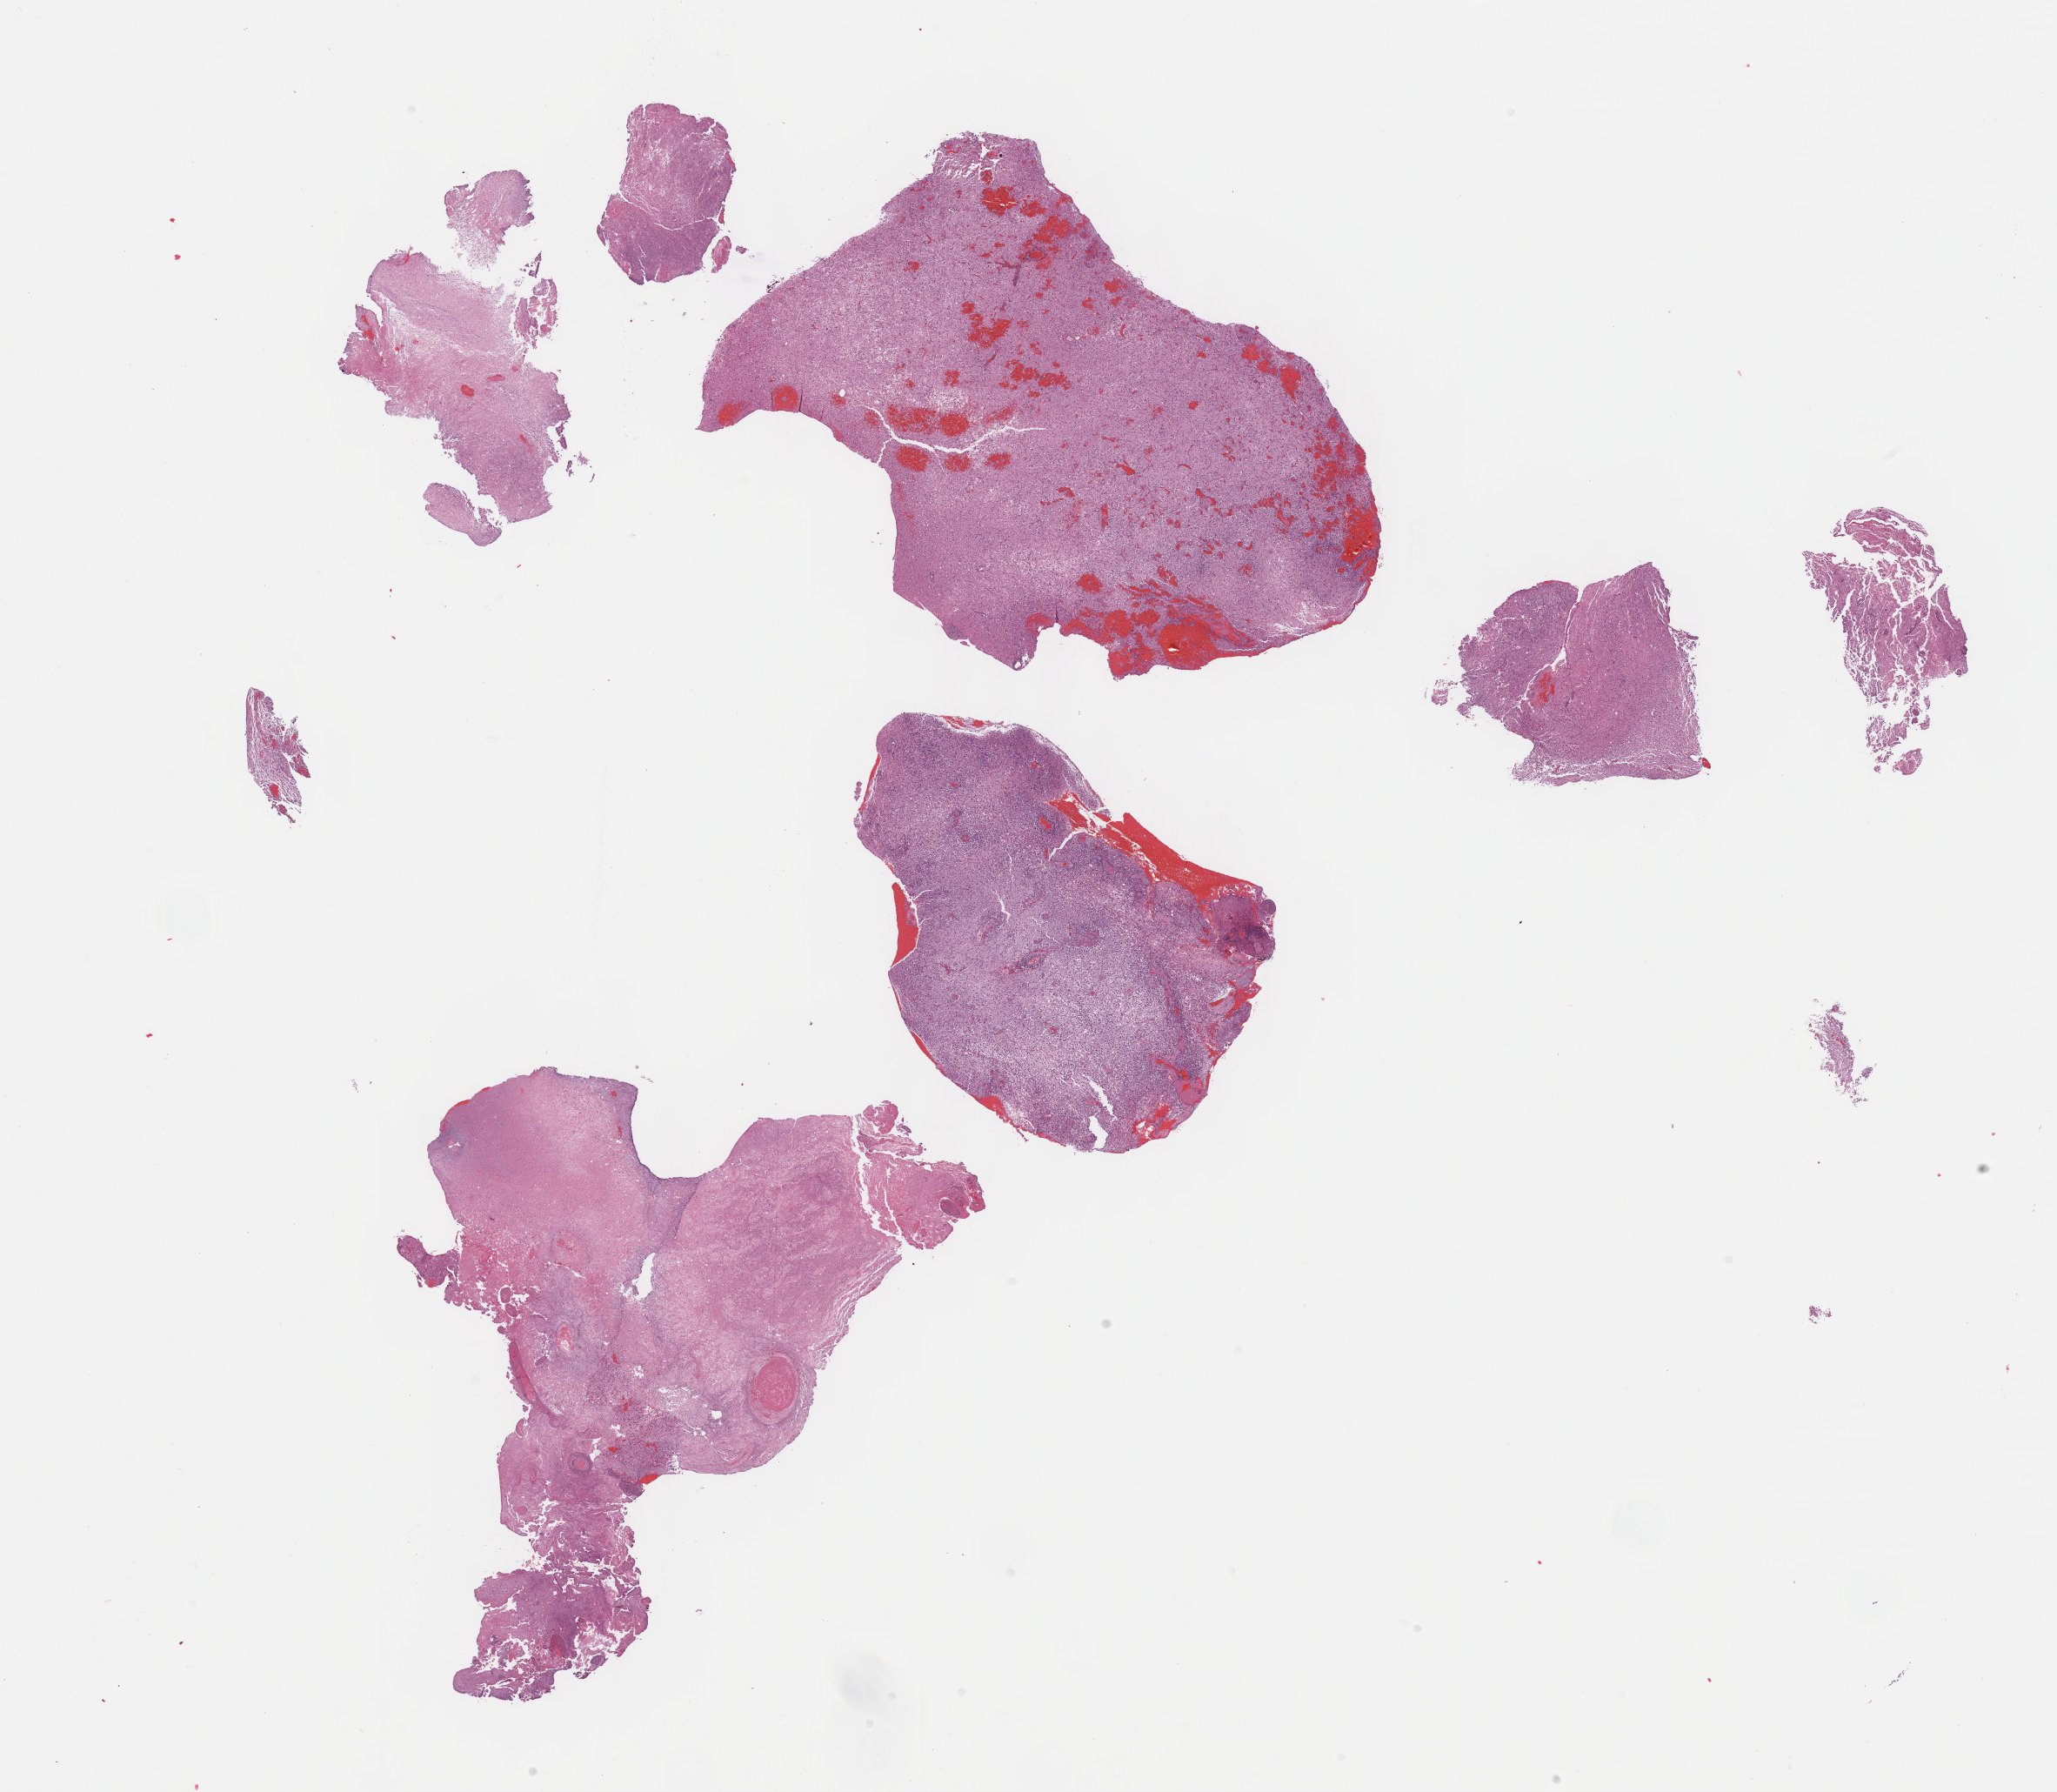
Whole-slide histology image, Hematoxylin and eosin (H&E) stained, a low-resolution overview of the entire scanned area, about 19.1 x 16.7 mm. Formalin-fixed paraffin-embedded (FFPE) diagnostic section. Sample: primary tumour, brain. Female patient; age at initial diagnosis 72 years.
Diagnosis: Glioblastoma (frontal lobe).